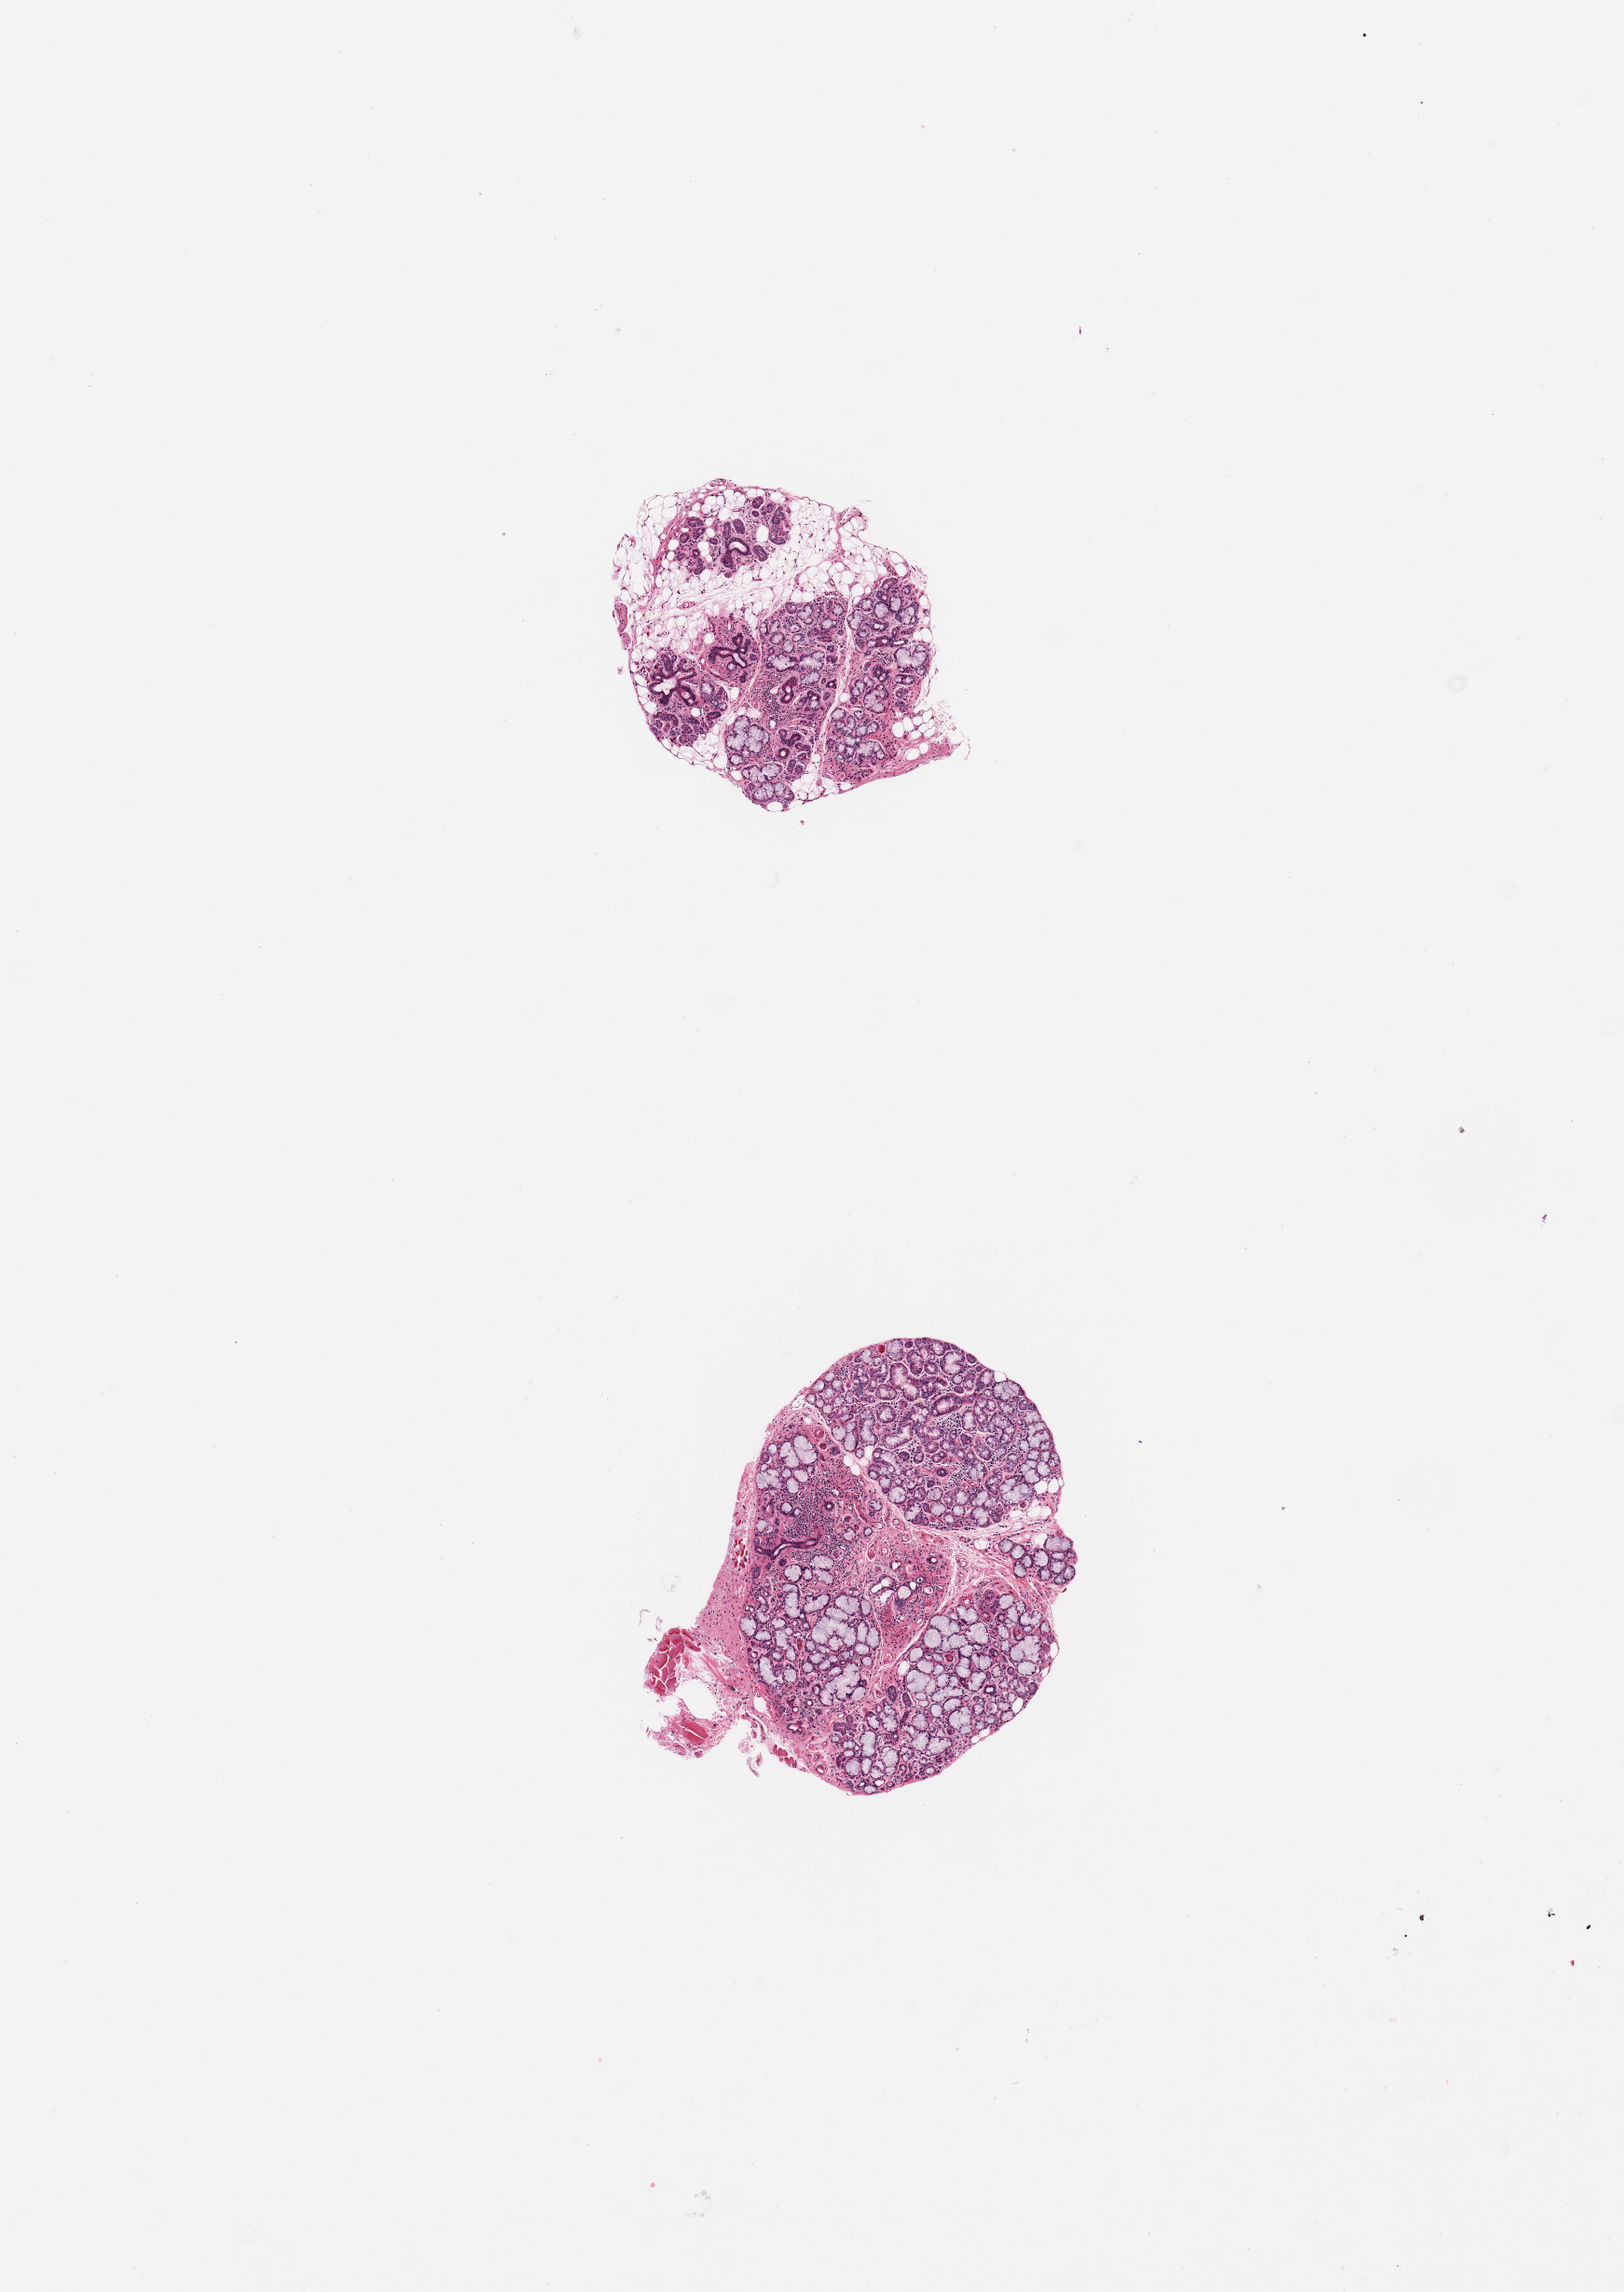
Digitized hematoxylin and eosin (H&E)-stained section, brightfield, a low-resolution overview of the entire scanned area, about 6.9 x 9.7 mm (slide scanned at 20x), PAXgene-fixed paraffin-embedded (PFPE) section, sampled site (target tissue): minor salivary gland, tissue donor sample. Donor sex: female.
Review note (as recorded): 2 pieces; well dissected; focal atrophy & lymphoid infiltrate; smaller piece has 25% fat content.